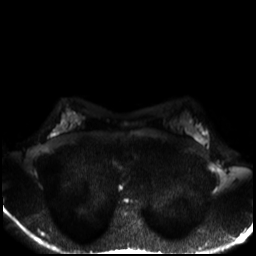
Breast MRI, one axial slice; slice 19 of 30 in the series (ordered by position); diffusion-weighted series; image 2 of 4 stored at this slice position (different b-values; order by instance number); 3 T; 4 mm slice thickness; 256 × 256 image matrix, field of view 320 × 320 mm. Female patient.
Structures marked on this image (outlined manually by an expert reader):
- tumour on diffusion-weighted imaging: box from (x=193, y=131) to (x=201, y=143) px